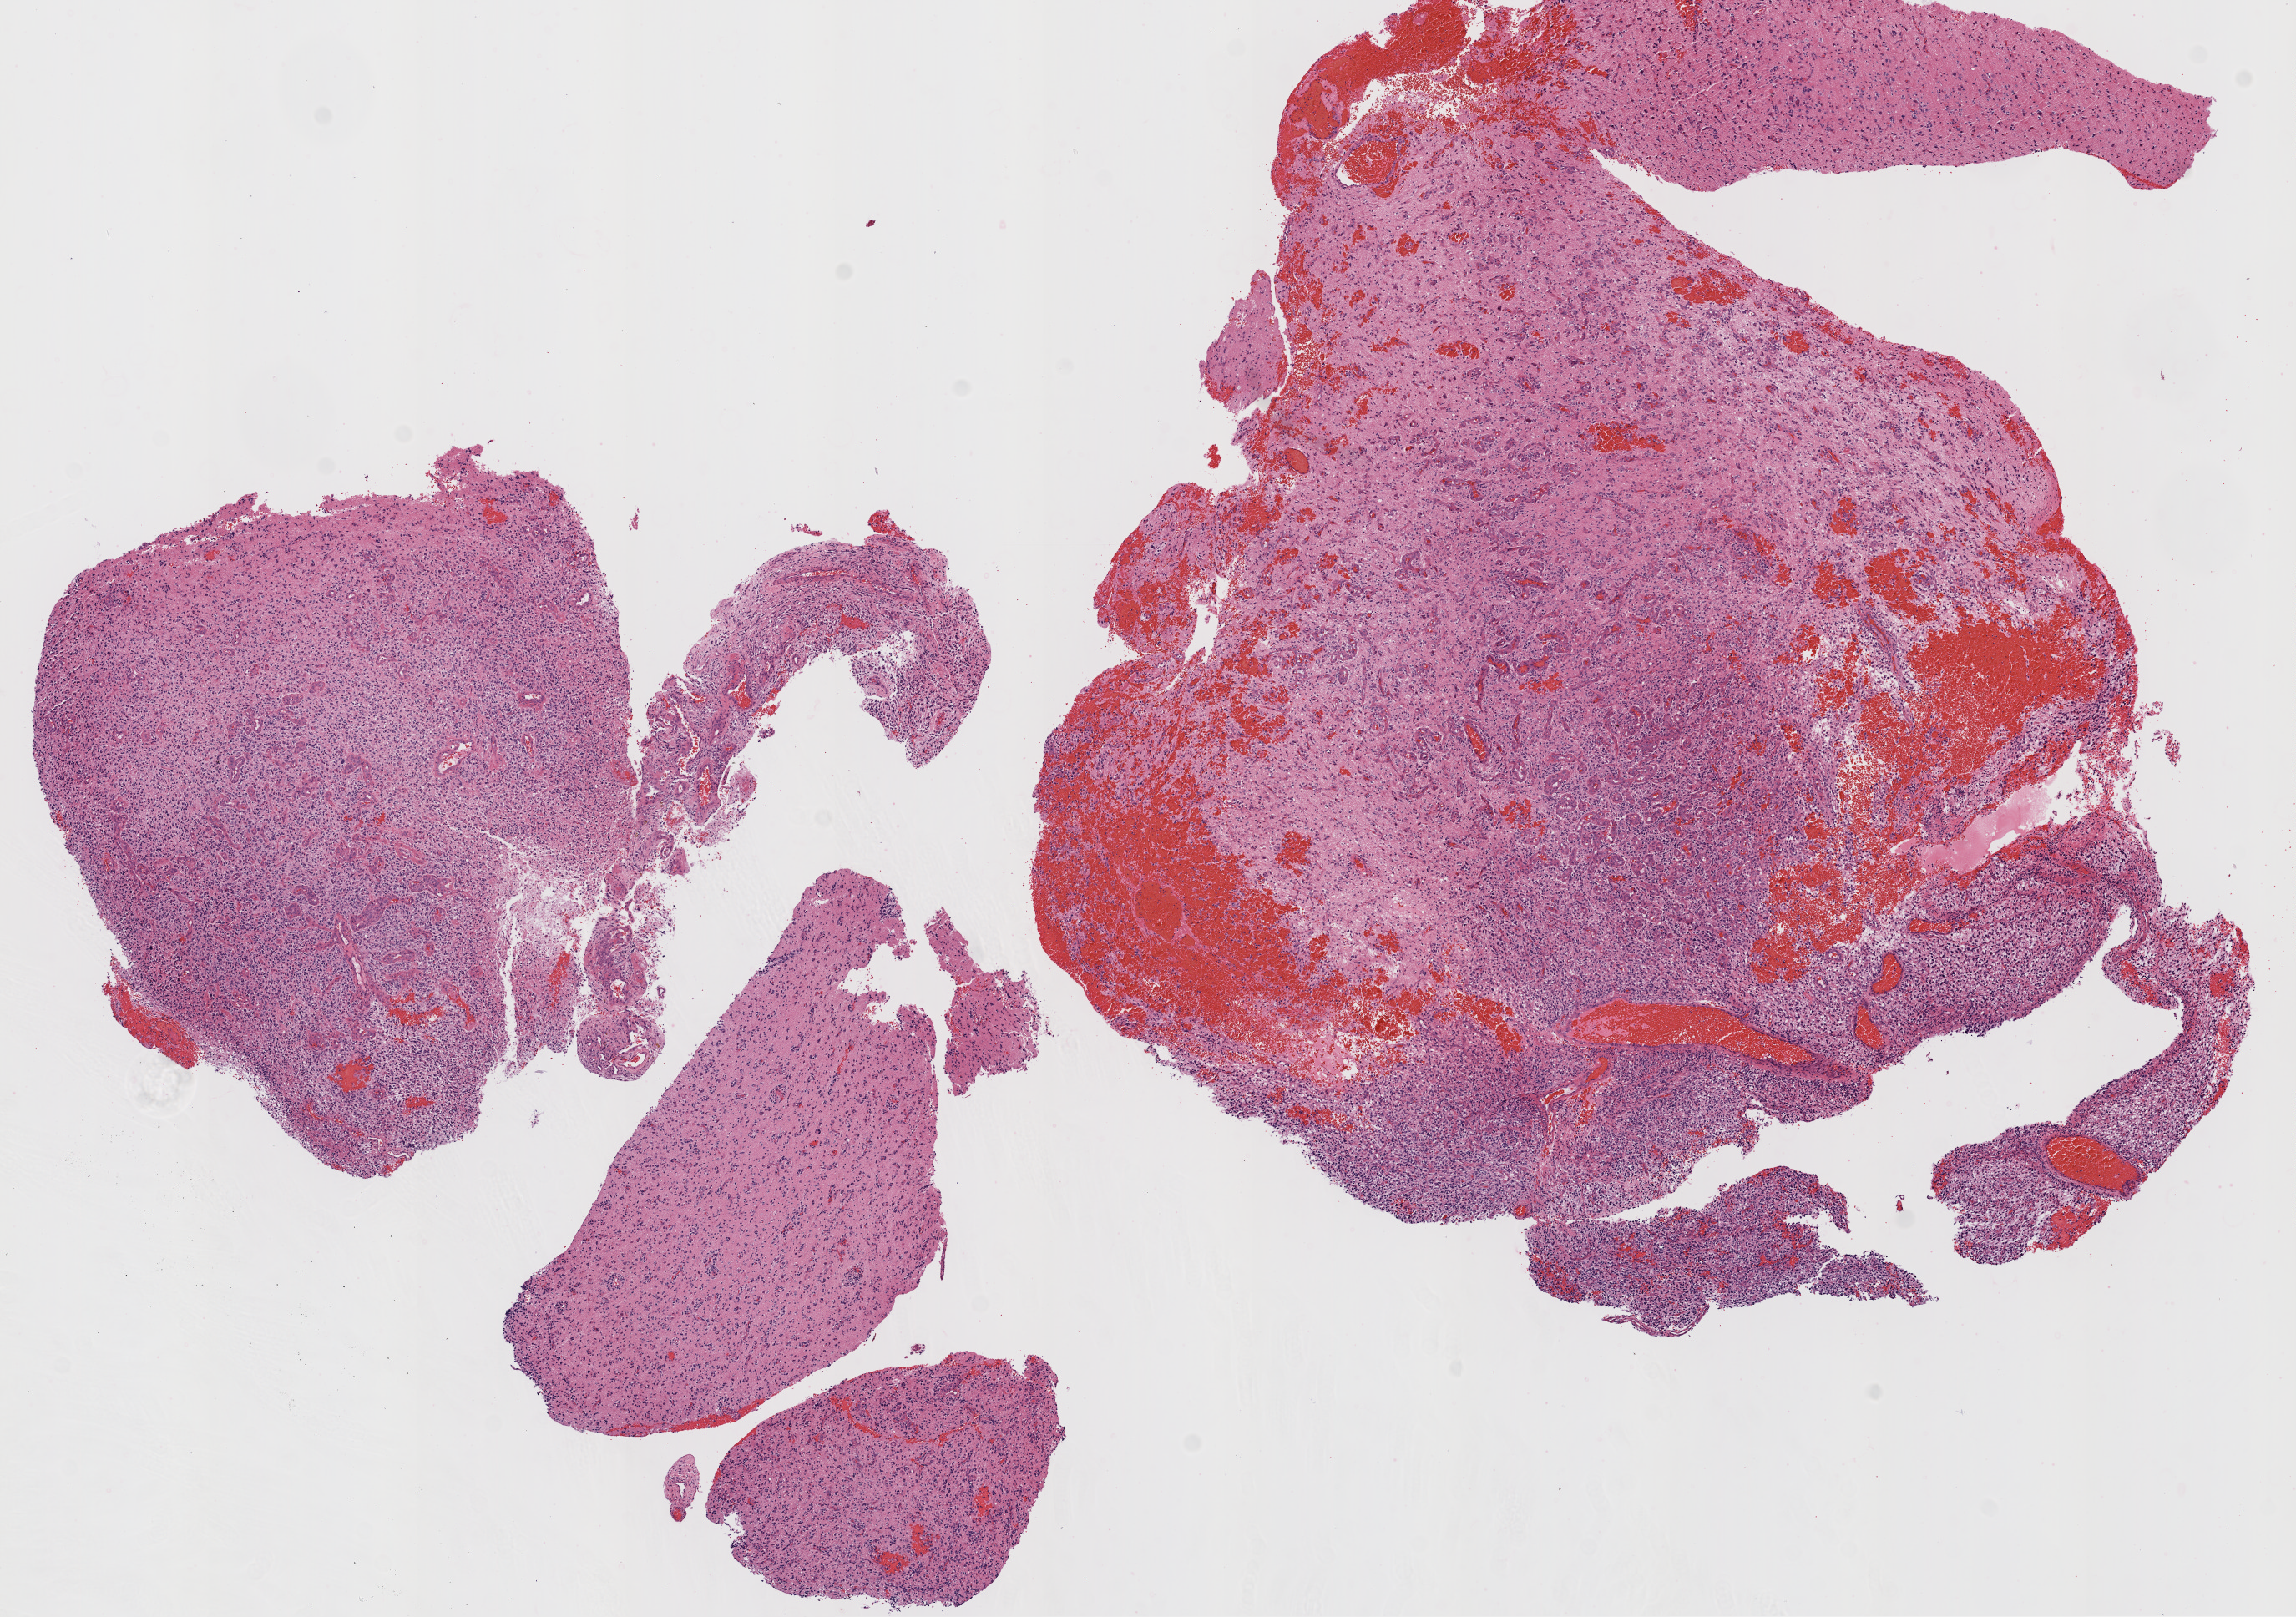
Whole-slide histology image, H&E, low-resolution overview of the scanned area, about 11.0 x 7.8 mm (acquisition: 20x scan). FFPE section. Brain, primary tumour sample. Patient: male, age at initial diagnosis 54 years.
- pathologic diagnosis: Glioblastoma